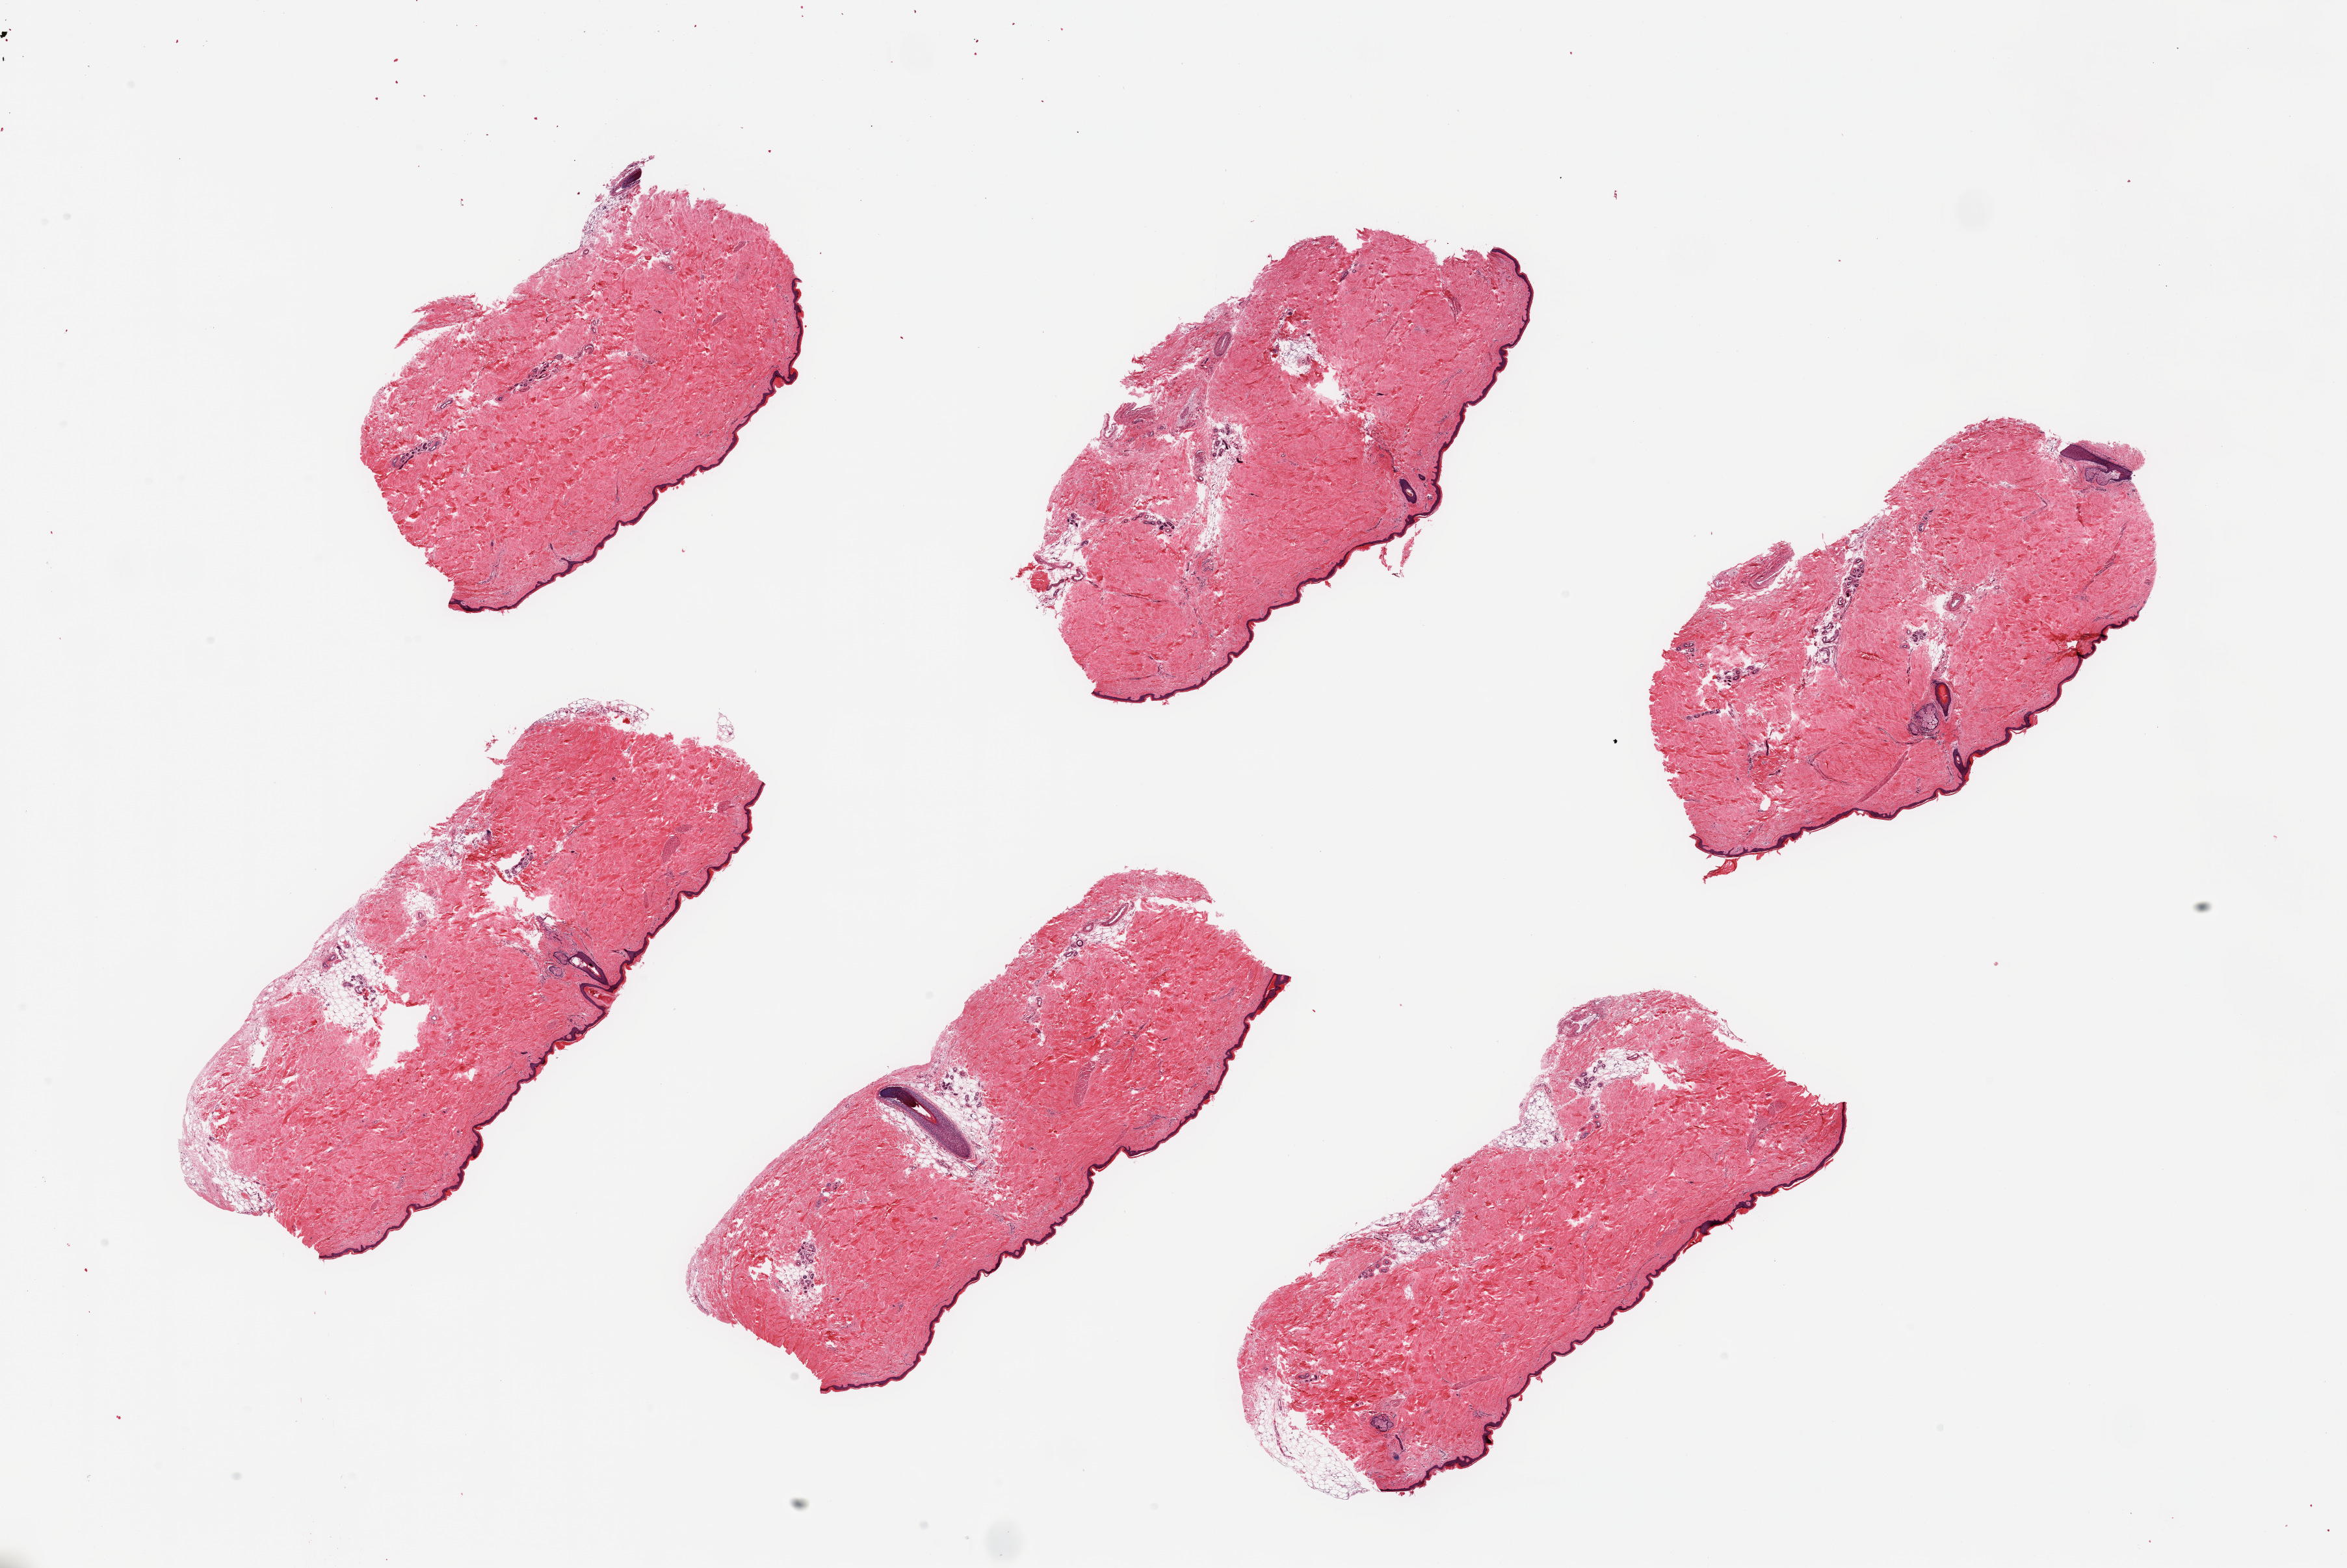
Whole-slide image, H&E stain — shown as a low-resolution overview of the whole scanned area (about 28.5 x 19.1 mm, slide scanned at 20x), PAXgene-fixed paraffin-embedded (PFPE) section, section of skin of lower leg (target tissue), donor tissue sample. Donor: male.
Reviewer comment on this tissue sample: 6 pieces, no dermal fat; squamous epithelium is ~30 microns.